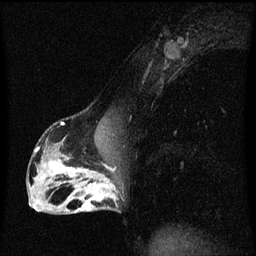
Breast MRI (dynamic contrast-enhanced), one sagittal slice; dynamic contrast-enhanced series, image 2 of 3 at this slice position (ordered by acquisition); 1.5 T; TE 4.2 ms, TR 8.4 ms; 2 mm slice thickness; 256 × 256 image matrix, field of view 200 × 200 mm. Female patient, age 40 years.
Structures marked on this image (semi-automatic segmentation, software-assisted and operator-edited):
- analysis volume of interest (the breast-tissue region the enhancement analysis was run in; not a lesion): bounding box (x1, y1, x2, y2) in pixels: (76, 172, 119, 213)
- tumour enhancement mask (voxels above the 70 % enhancement threshold inside the analysis volume of interest): (79, 172, 117, 211)